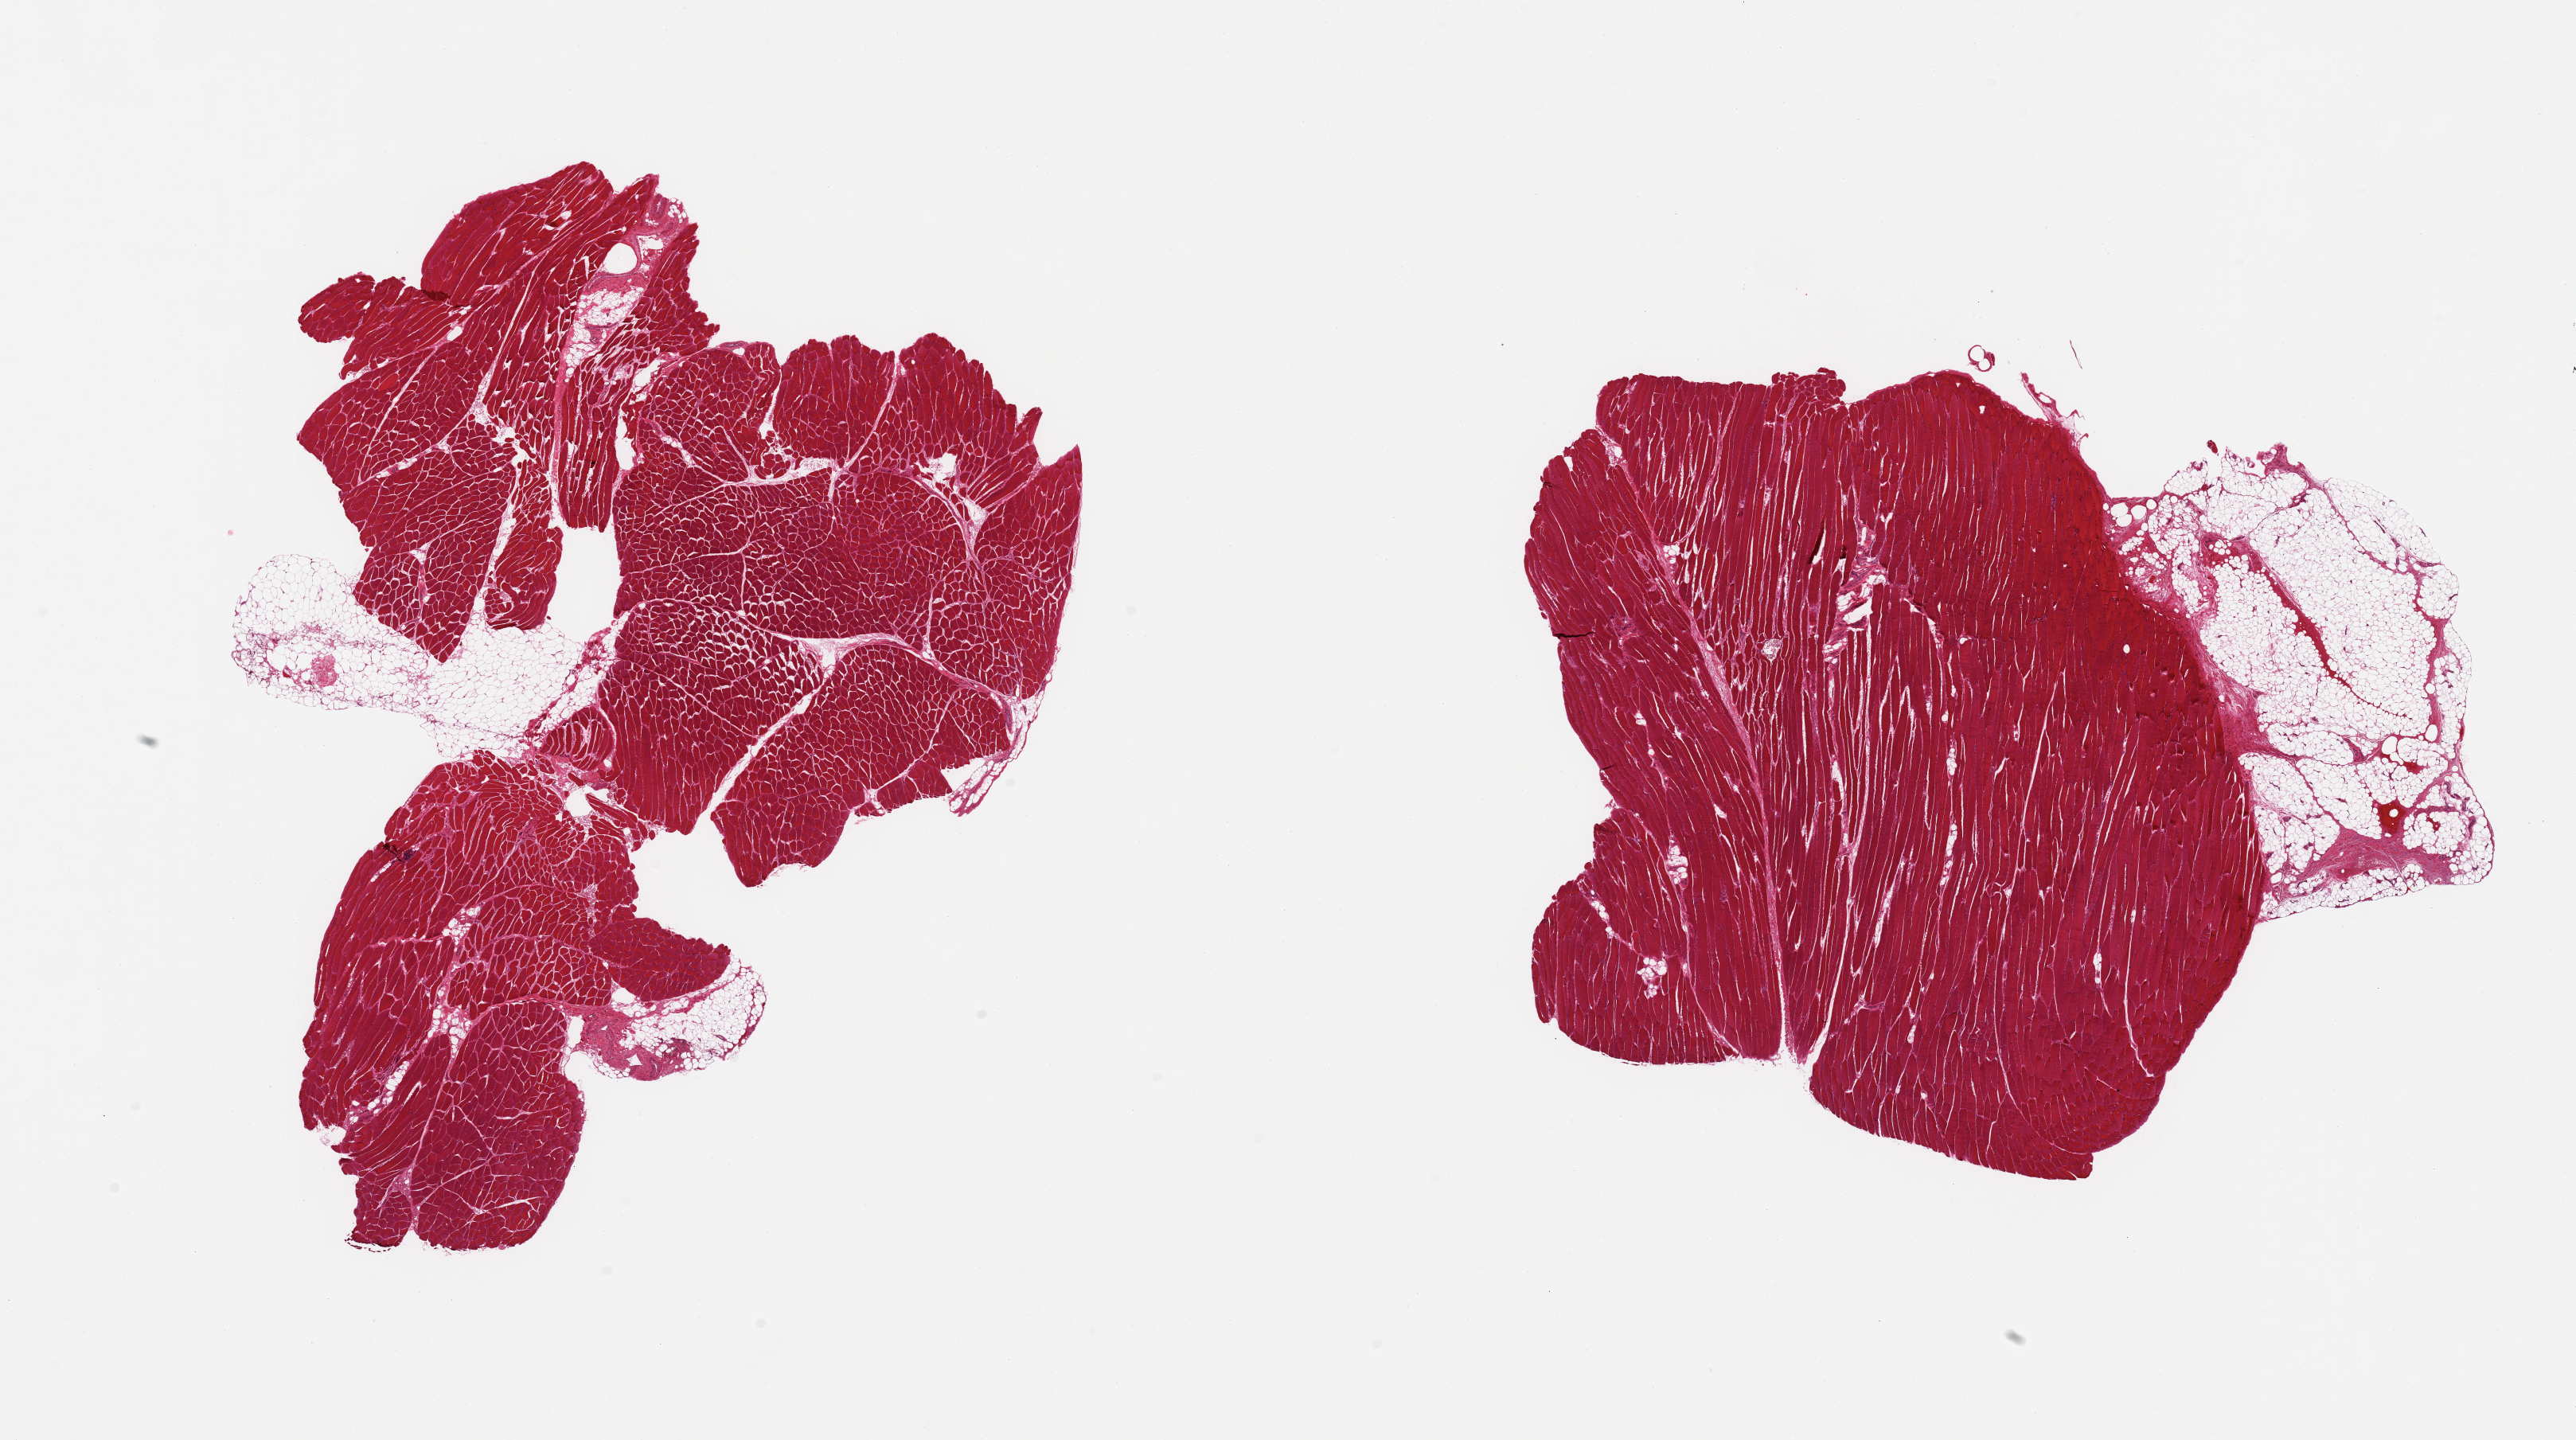
Digitized hematoxylin and eosin (H&E)-stained section, brightfield, a low-resolution overview of the entire scanned area, about 25.6 x 14.3 mm (from a 20x scan), PAXgene-fixed, paraffin-embedded tissue, section of skeletal muscle (target tissue), tissue donor sample. Male donor.
Pathologist's review note for this sample: 2 pieces, adherent/interstitial fat/vascular elements is ~20% of tissue.